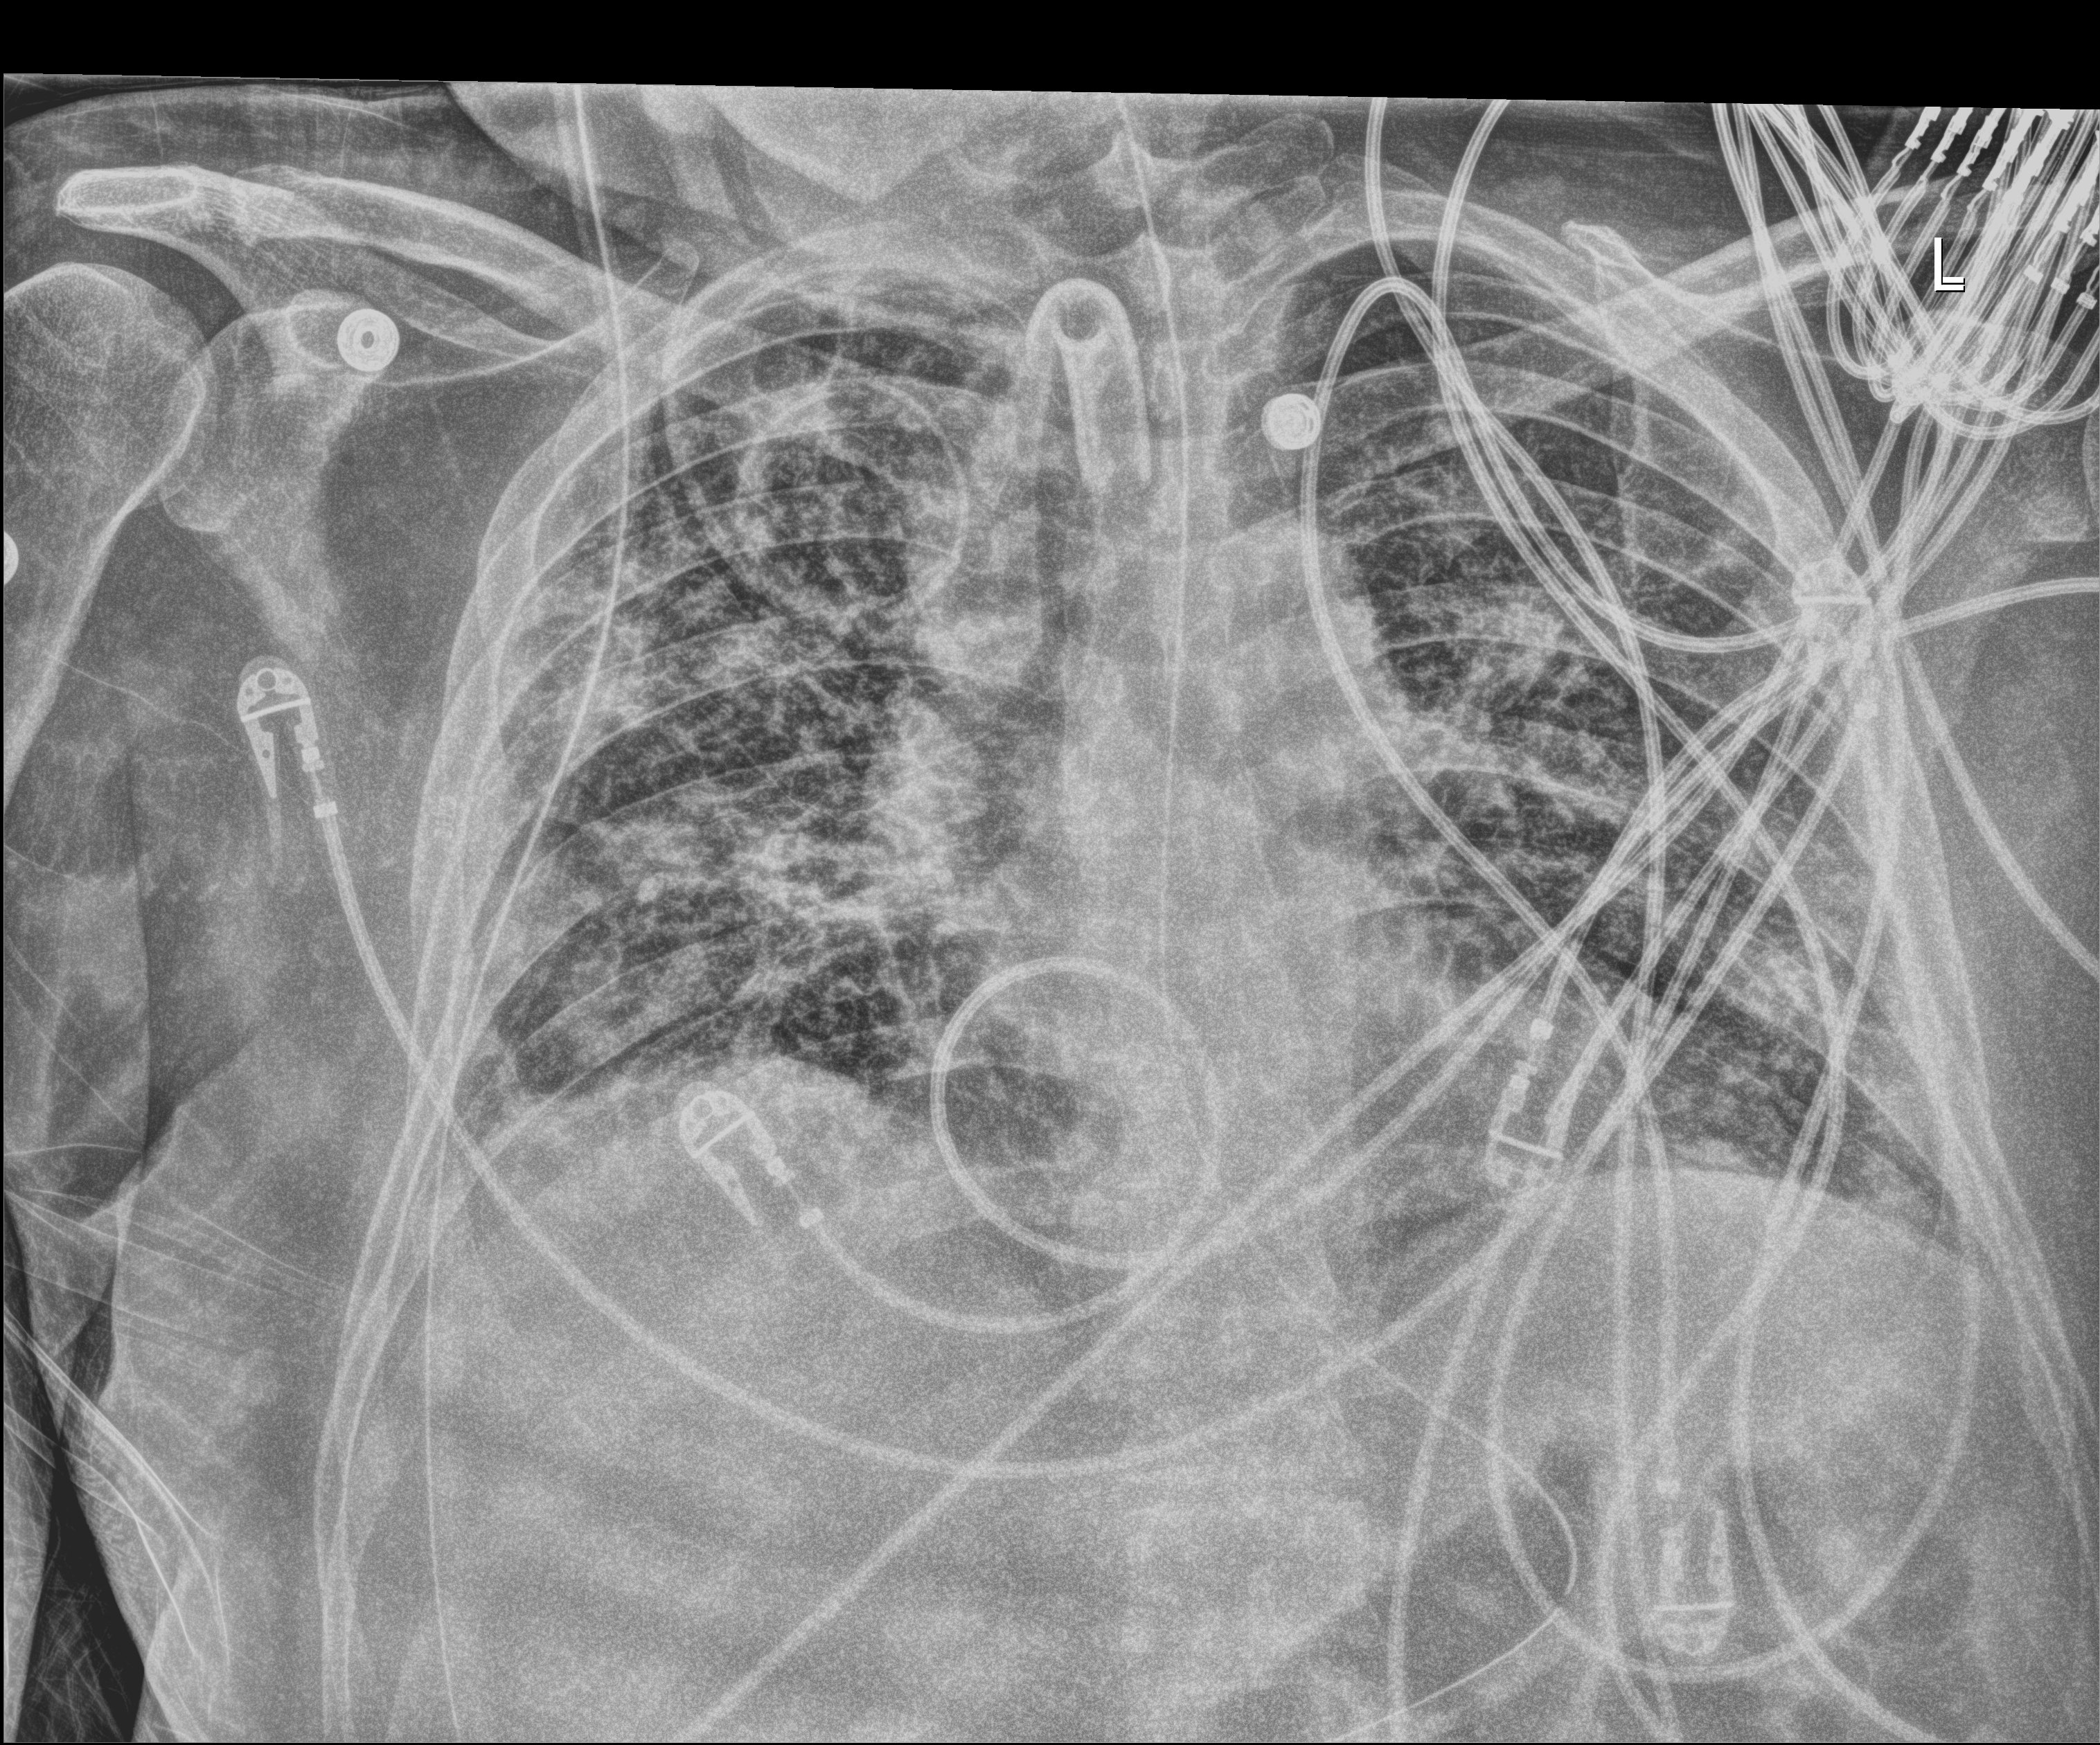
Portable chest radiograph, anteroposterior (AP) projection. Male patient hospitalised with COVID-19, age 18–59 years.
Hospital-stay facts (about this admission, not read from this image; timing relative to this image not recorded): length of hospital stay: 63 days.